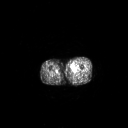
FDG PET of an extremity soft-tissue mass (from a PET/CT study), one axial slice; slice 229 of 267 in the series (ordered by position); 3.27 mm slice thickness; 128 × 128 image matrix, field of view 700 × 700 mm. Patient: male, 48 years. Case-level facts recorded for this patient, not image findings: histological type: pleiomorphic leiomyosarcoma; grade: high; site of the primary tumour: left thigh.
Structures marked on this image (expert contour drawn on MRI and transferred to this co-registered scan by the dataset authors):
- gross tumour volume including surrounding oedema: bounding box [x1, y1, x2, y2] px = [69, 63, 75, 71]
- gross tumour volume (mass): [70, 66, 74, 70]